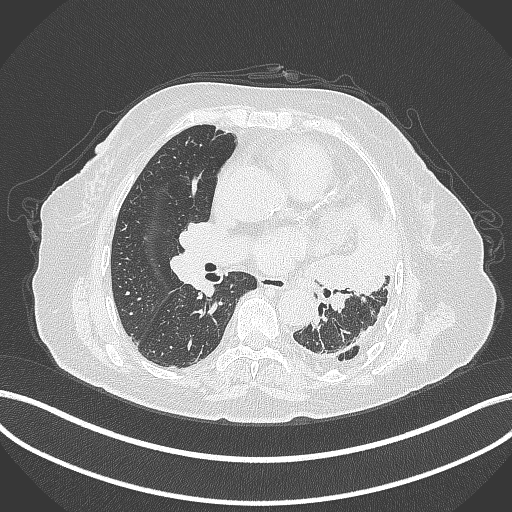
Chest CT, one axial slice. Slice 190 of 399 in the series (ordered by position). Reconstruction kernel B70f. 120 kVp. Lung window (W 1500 / L -600 HU). 512 × 512 image matrix, field of view 400 × 400 mm. Female patient, age 75 years. From the clinical record (not read from this slice): clinical TNM (as recorded): T3 N3 M1.
Annotated regions visible in this slice (bounding box drawn by a radiologist):
- lung tumour (recorded histology: adenocarcinoma): bounding box (x1, y1, x2, y2) in pixels: (304, 216, 393, 300)